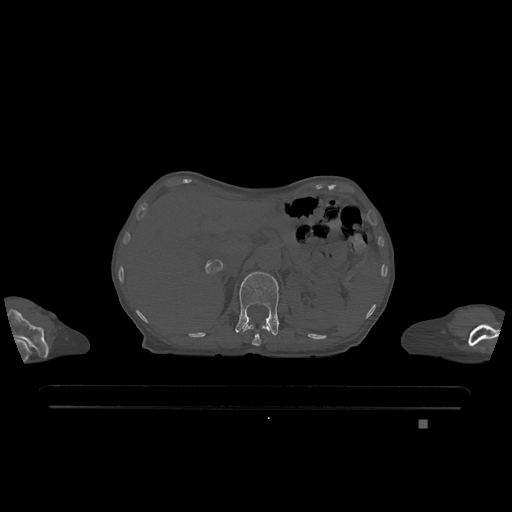
CT including the spine, one axial slice. Slice 491 of 1317 in the series (ordered by position). Bone window (W 1800 / L 400 HU). 0.5 mm slice thickness. 512 × 512 image matrix, field of view 500 × 500 mm. Patient: female, 74 years. From the clinical record (not read from this slice): primary cancer: lung.
Outlined on this slice (semi-automatically segmented with operator editing):
- L1 vertebra: bounding box <235,272,279,336> (left, top, right, bottom; pixels)
- T12 vertebra: <243,324,270,346>